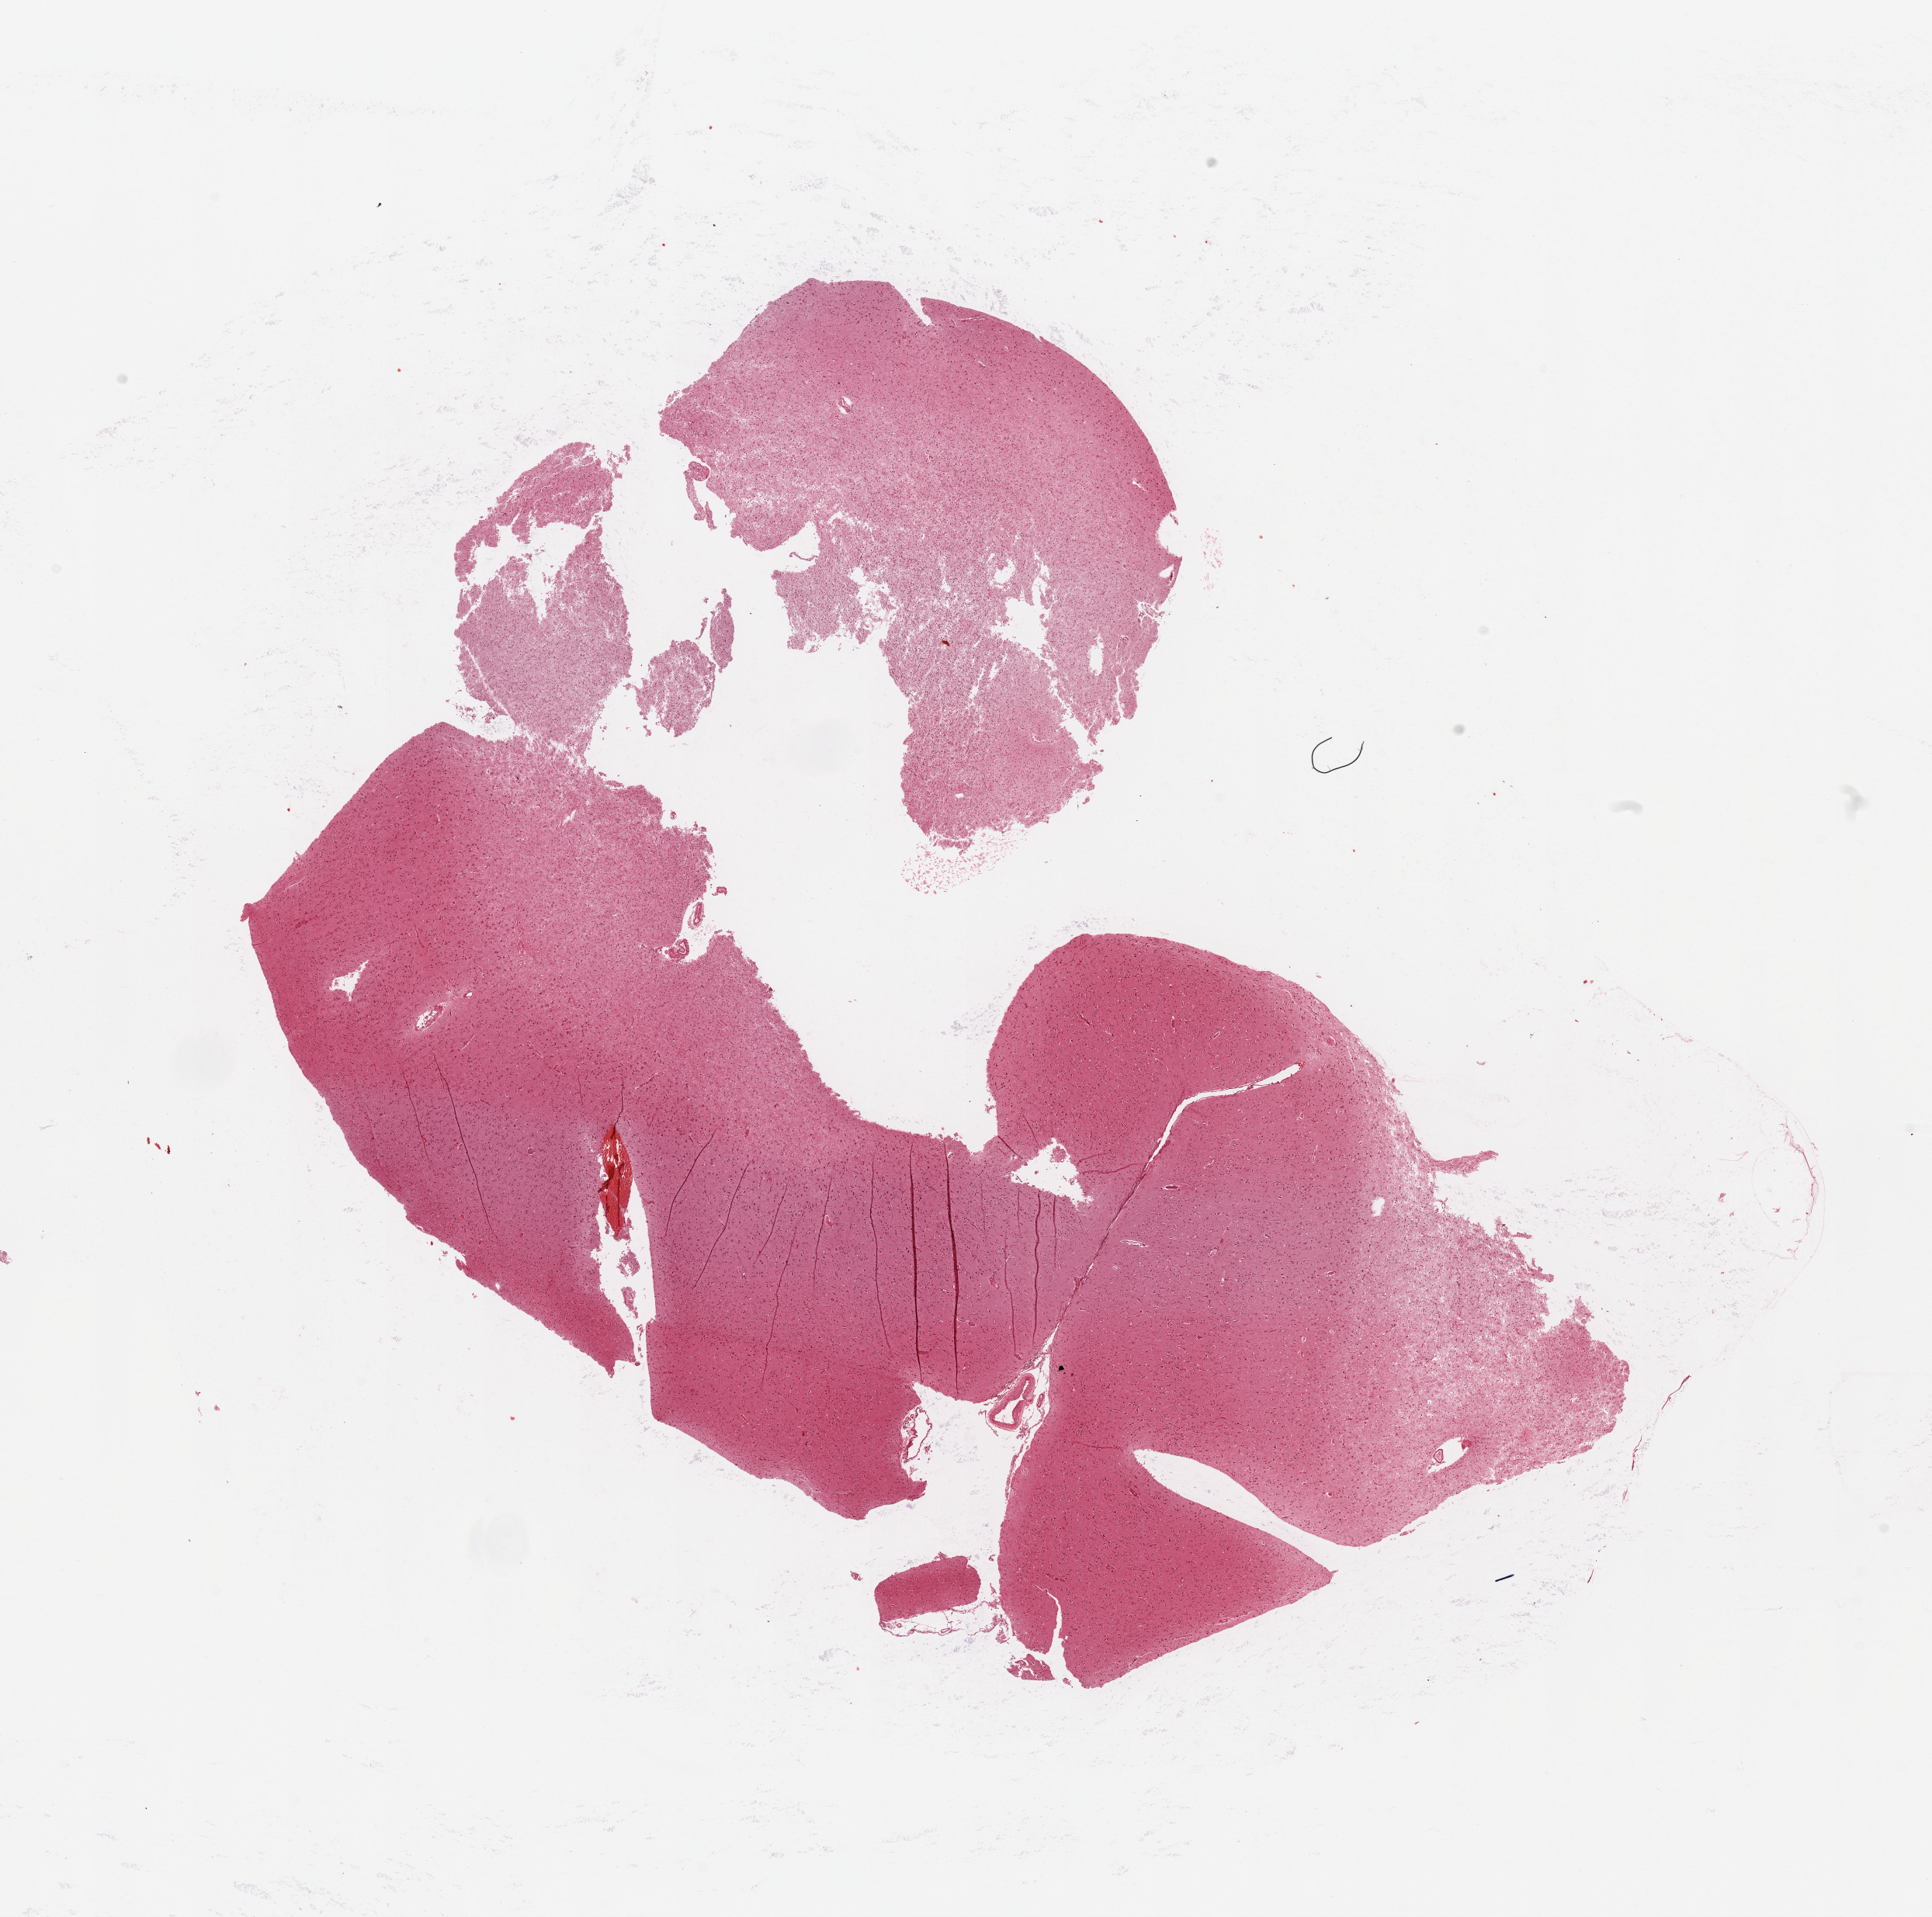
Whole-slide histology image, Hematoxylin and eosin (H&E) stained — shown as a low-resolution overview of the whole scanned area (about 19.7 x 19.5 mm, from a 20x scan). Tumour tissue sample, brain. 62-year-old female patient.
Patient diagnosis (cohort enrolment): glioblastoma multiforme (brain). Primary tumour site (as recorded): parietal lobe.